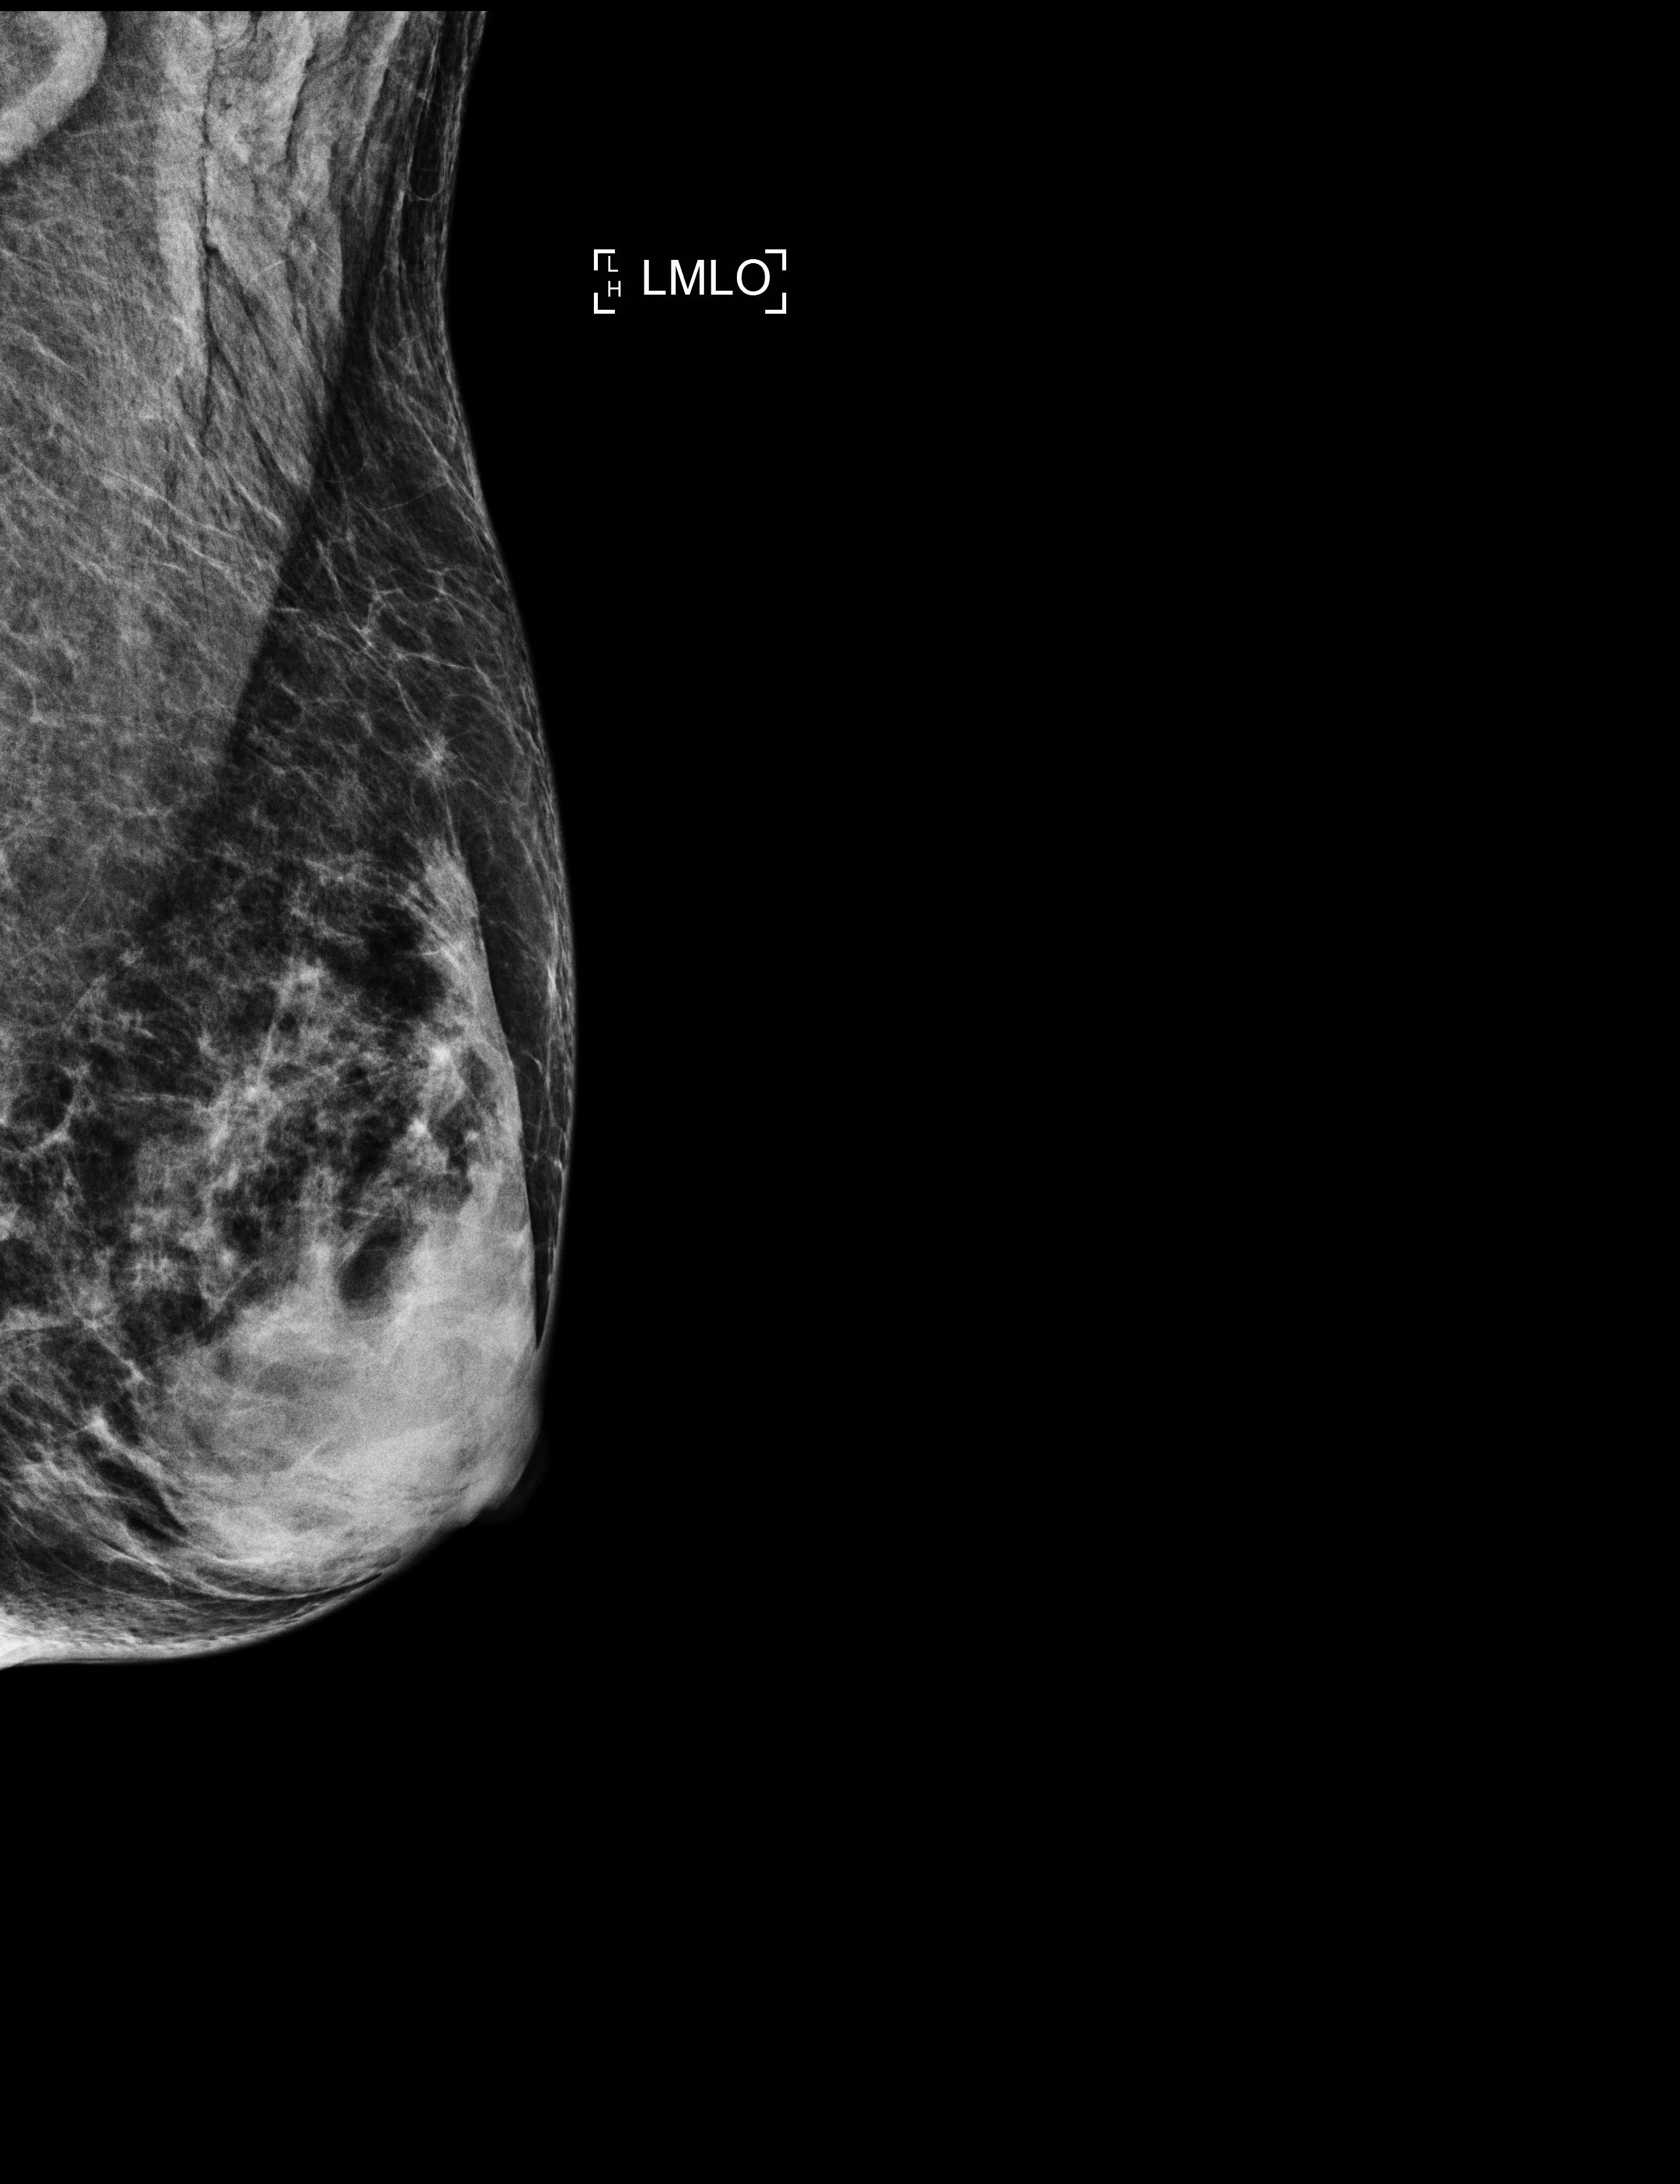
Annual screening mammography examination; compressed breast thickness 30 mm. Patient aged 67 years (female).
Image type: full-field digital mammogram. Breast: left. Projection: medio-lateral oblique projection.